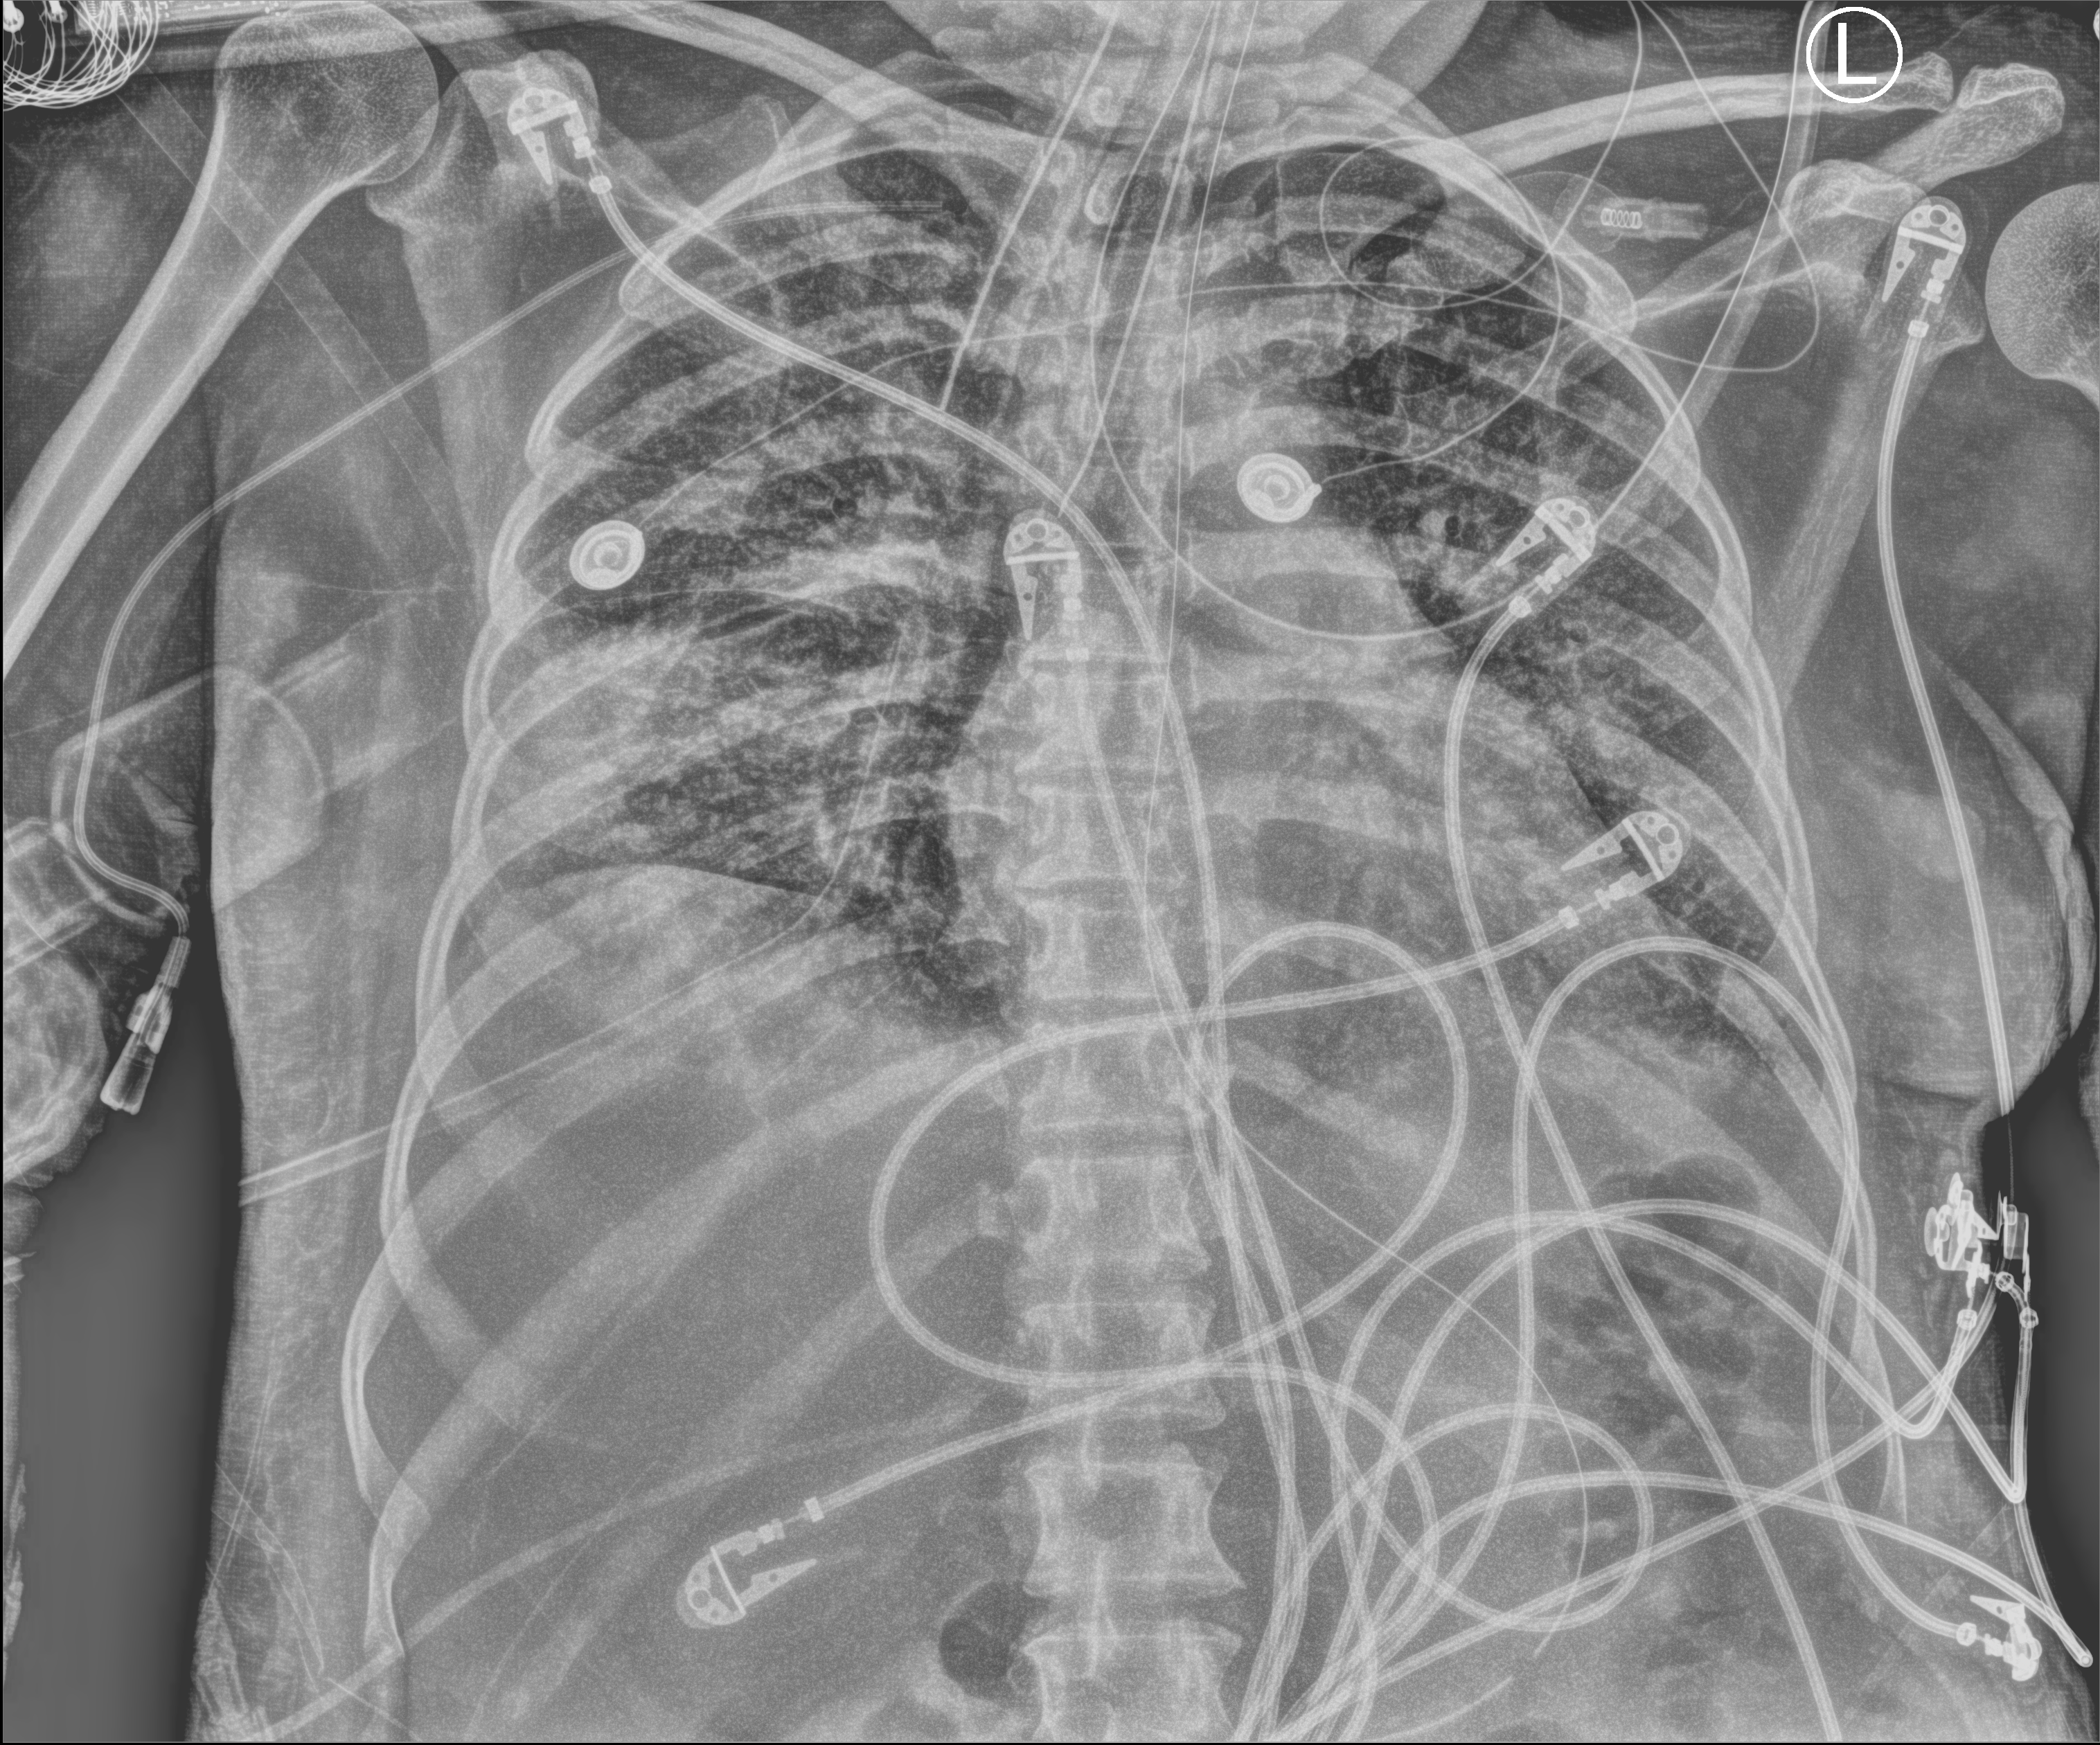
Portable chest radiograph; anteroposterior (AP) projection. Patient hospitalised with COVID-19; female, aged 18–59 years.
Admission-level facts for this patient (not findings on this image; timing relative to this image not recorded):
- other chronic lung disease (admission record): no
- chronic kidney disease (admission record): no
- admitted to intensive care during this hospital stay: yes